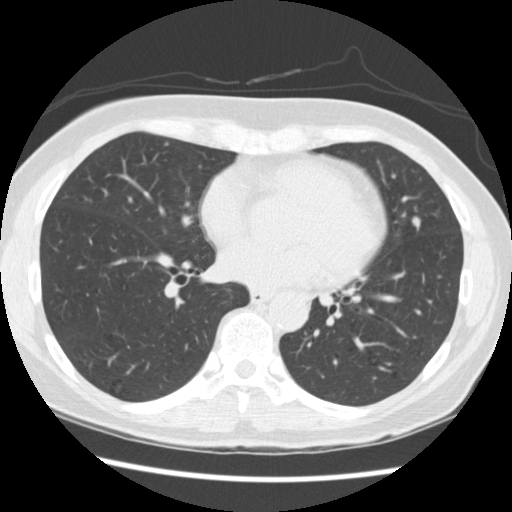
Low-dose screening chest CT, one axial slice; slice 121 of 262 in the series (ordered by position); reconstruction kernel STANDARD; 120 kVp; lung window (W 1500 / L -600 HU); 2.5 mm slice thickness; 512 × 512 image matrix.
Outlined on this slice (expert manual segmentation):
- lesion 2 (tumor, lingular bronchus): bounding box [x1, y1, x2, y2] px = [412, 216, 421, 226]